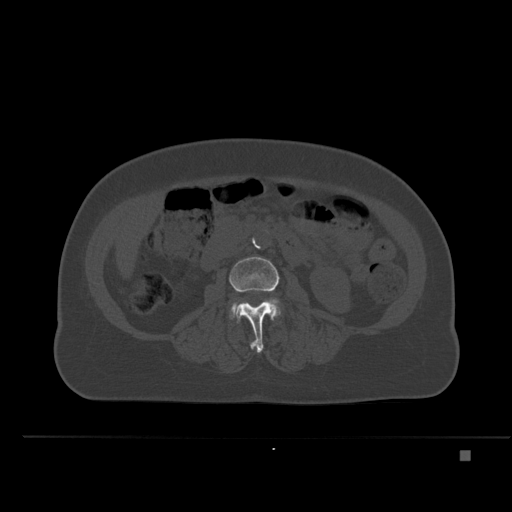
CT including the spine, one axial slice. Slice 194 of 477 in the series (ordered by position). Bone window (W 1800 / L 400 HU). 1.5 mm slice thickness. 512 × 512 image matrix, field of view 422 × 422 mm. Patient: female, 74 years. Case-level facts recorded for this patient, not image findings: primary cancer: colon.
Structures marked on this image (semi-automatic segmentation, software-assisted and operator-edited):
- L3 vertebra: bounding box (x1, y1, x2, y2) in pixels: (229, 257, 280, 353)
- L4 vertebra: (231, 302, 279, 317)